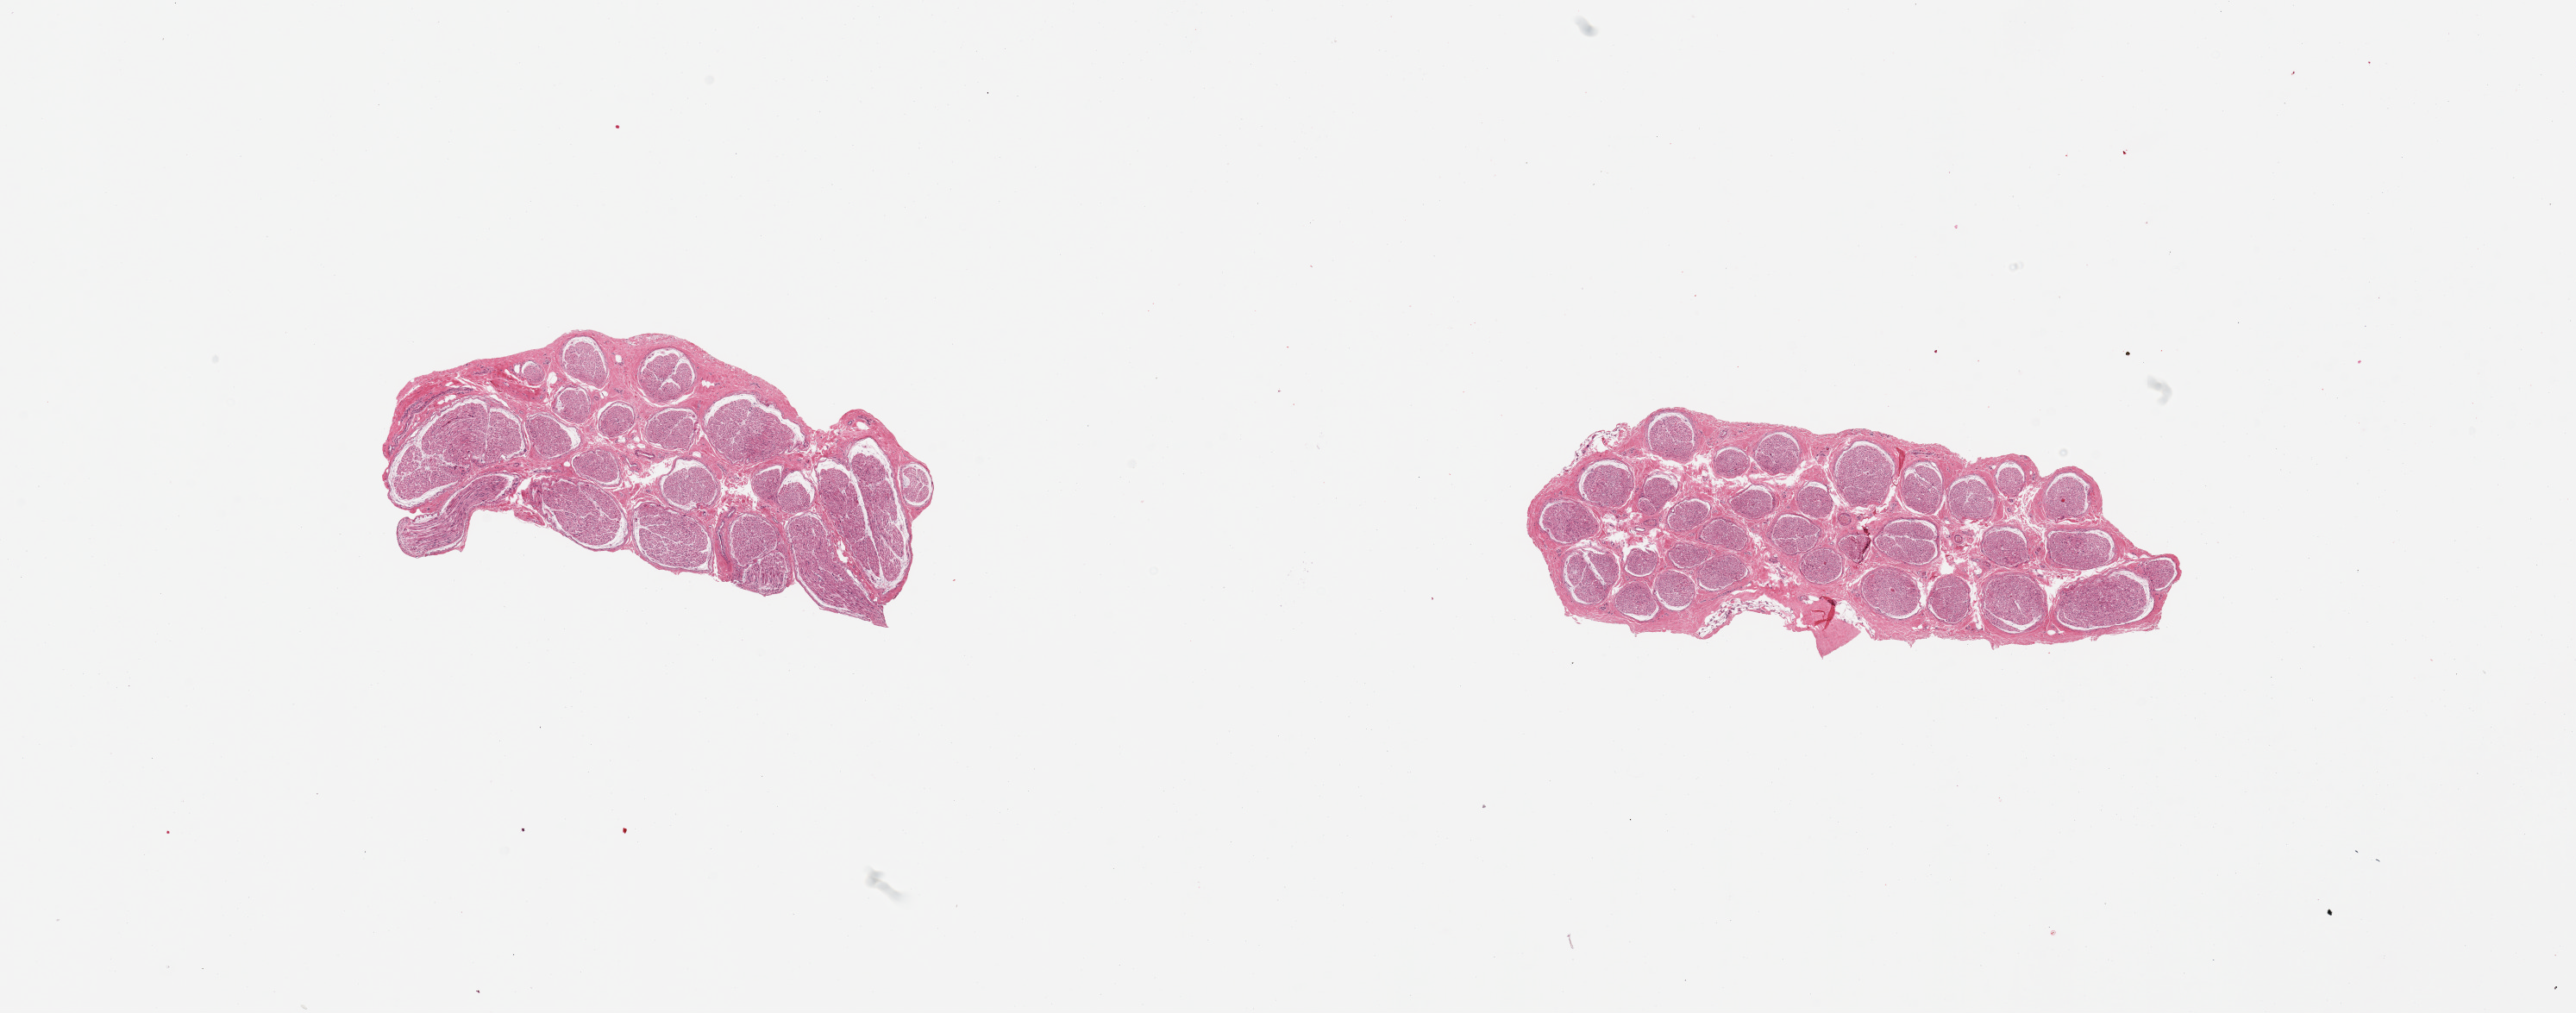
Whole-slide image, haematoxylin and eosin stain — low-resolution overview of the scanned area, about 23.6 x 9.3 mm, PAXgene-fixed, paraffin-embedded tissue, target tissue: tibial nerve, tissue donor sample.
Pathologist's review note for this sample: 2 pieces; well trimmed; no lesions.